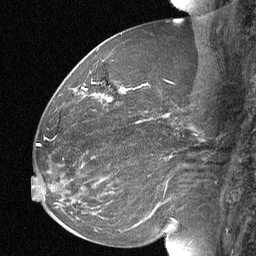
Breast MRI (dynamic contrast-enhanced), one sagittal slice; slice 29 of 64 in the series (ordered by position); dynamic contrast-enhanced study with each time point stored as its own series, time point 2 of 3 at this slice position (early post-contrast, ordered by acquisition time); 1.5 T; TE 4.8 ms, TR 27 ms; 2 mm slice thickness; 256 × 256 image matrix, field of view 200 × 200 mm. Patient: female, 60 years. Case-level facts recorded for this patient, not image findings: setting: breast cancer imaged before/during neoadjuvant chemotherapy; receptor status: HR-positive, HER2-negative.
Structures marked on this image (semi-automatic segmentation, software-assisted and operator-edited):
- analysis volume of interest (the breast-tissue region the enhancement analysis was run in; not a lesion): bounding box <92,70,125,108> (left, top, right, bottom; pixels)
- tumour enhancement mask (voxels above the 90 % enhancement threshold inside the analysis volume of interest): <108,98,111,101>